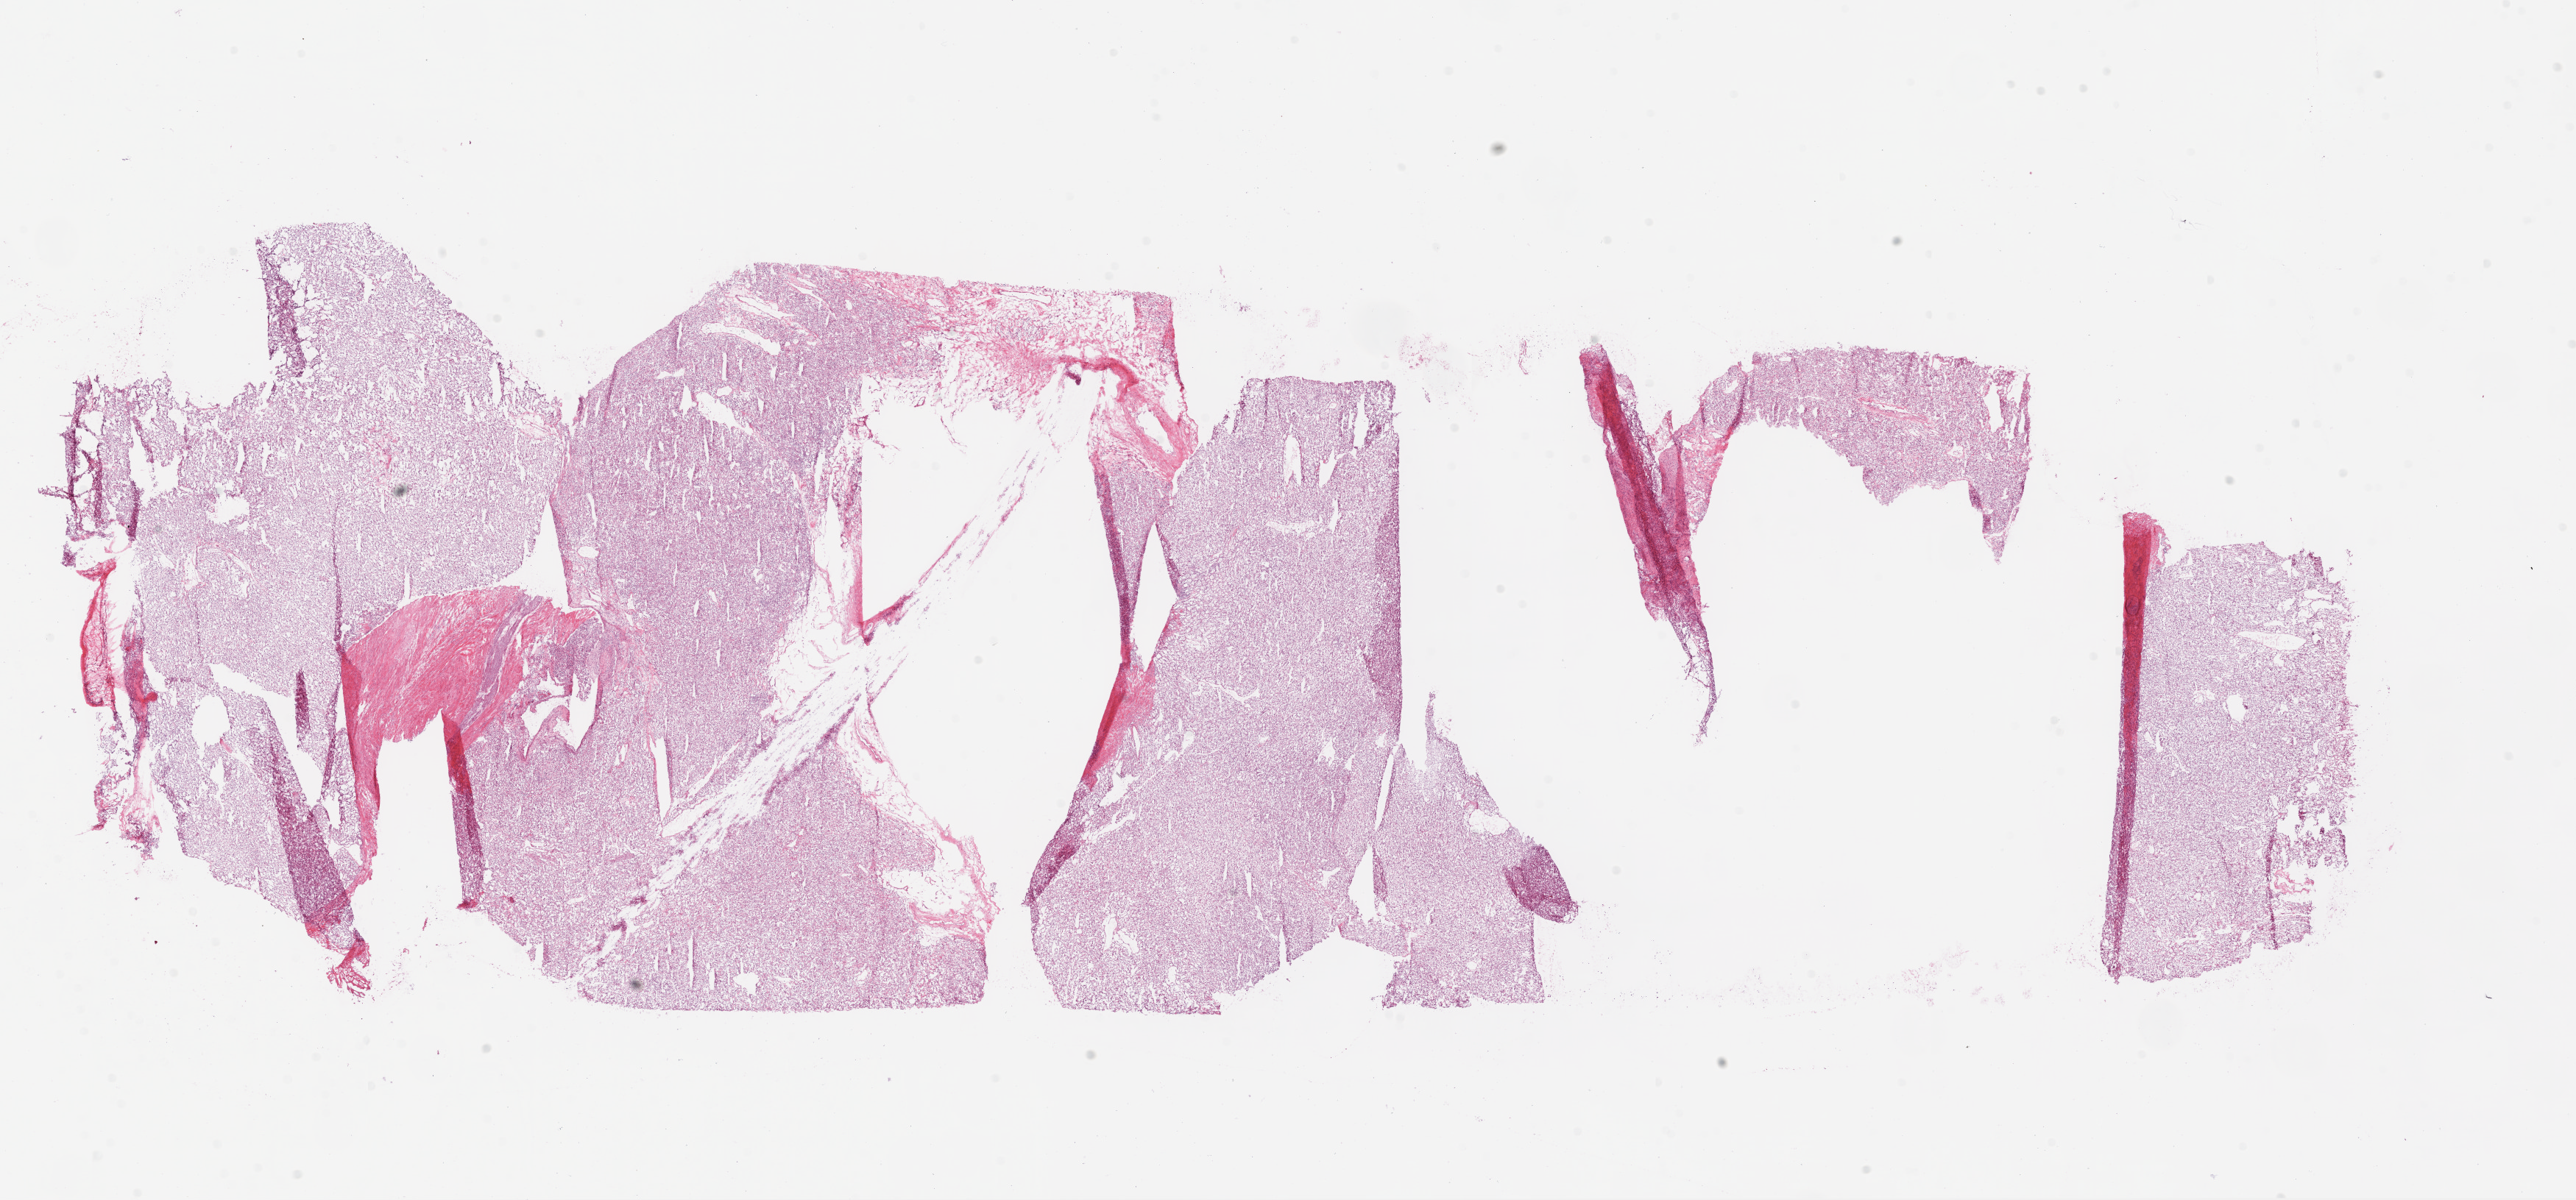
Whole-slide histology image, H&E, a low-resolution overview of the entire scanned area, about 28.1 x 13.1 mm (from a 20x scan). Frozen section from the bottom of the tissue portion. Primary tumour sample from the kidney. Patient: female, age at initial diagnosis 67 years.
Pathologic diagnosis: Clear cell adenocarcinoma, NOS.